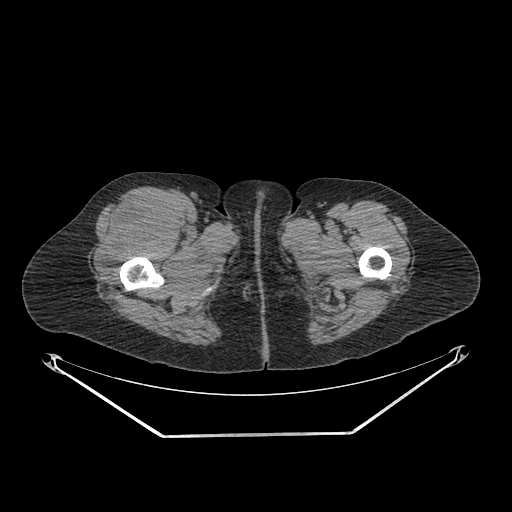
CT of an extremity soft-tissue mass (from a PET/CT study), one axial slice; reconstruction kernel SOFT; soft-tissue window (W 400 / L 40 HU); 512 × 512 image matrix, field of view 500 × 500 mm. Female patient. Case-level facts recorded for this patient, not image findings: histological type: pleiomorphic undifferentiated sarcoma; grade: high; site of the primary tumour: right quadricep.
Structures marked on this image (expert contour drawn on MRI and transferred to this co-registered scan by the dataset authors):
- tumour plus oedema (research contour): bounding box [x1, y1, x2, y2] px = [98, 196, 175, 271]
- tumour (research contour): [98, 196, 175, 271]